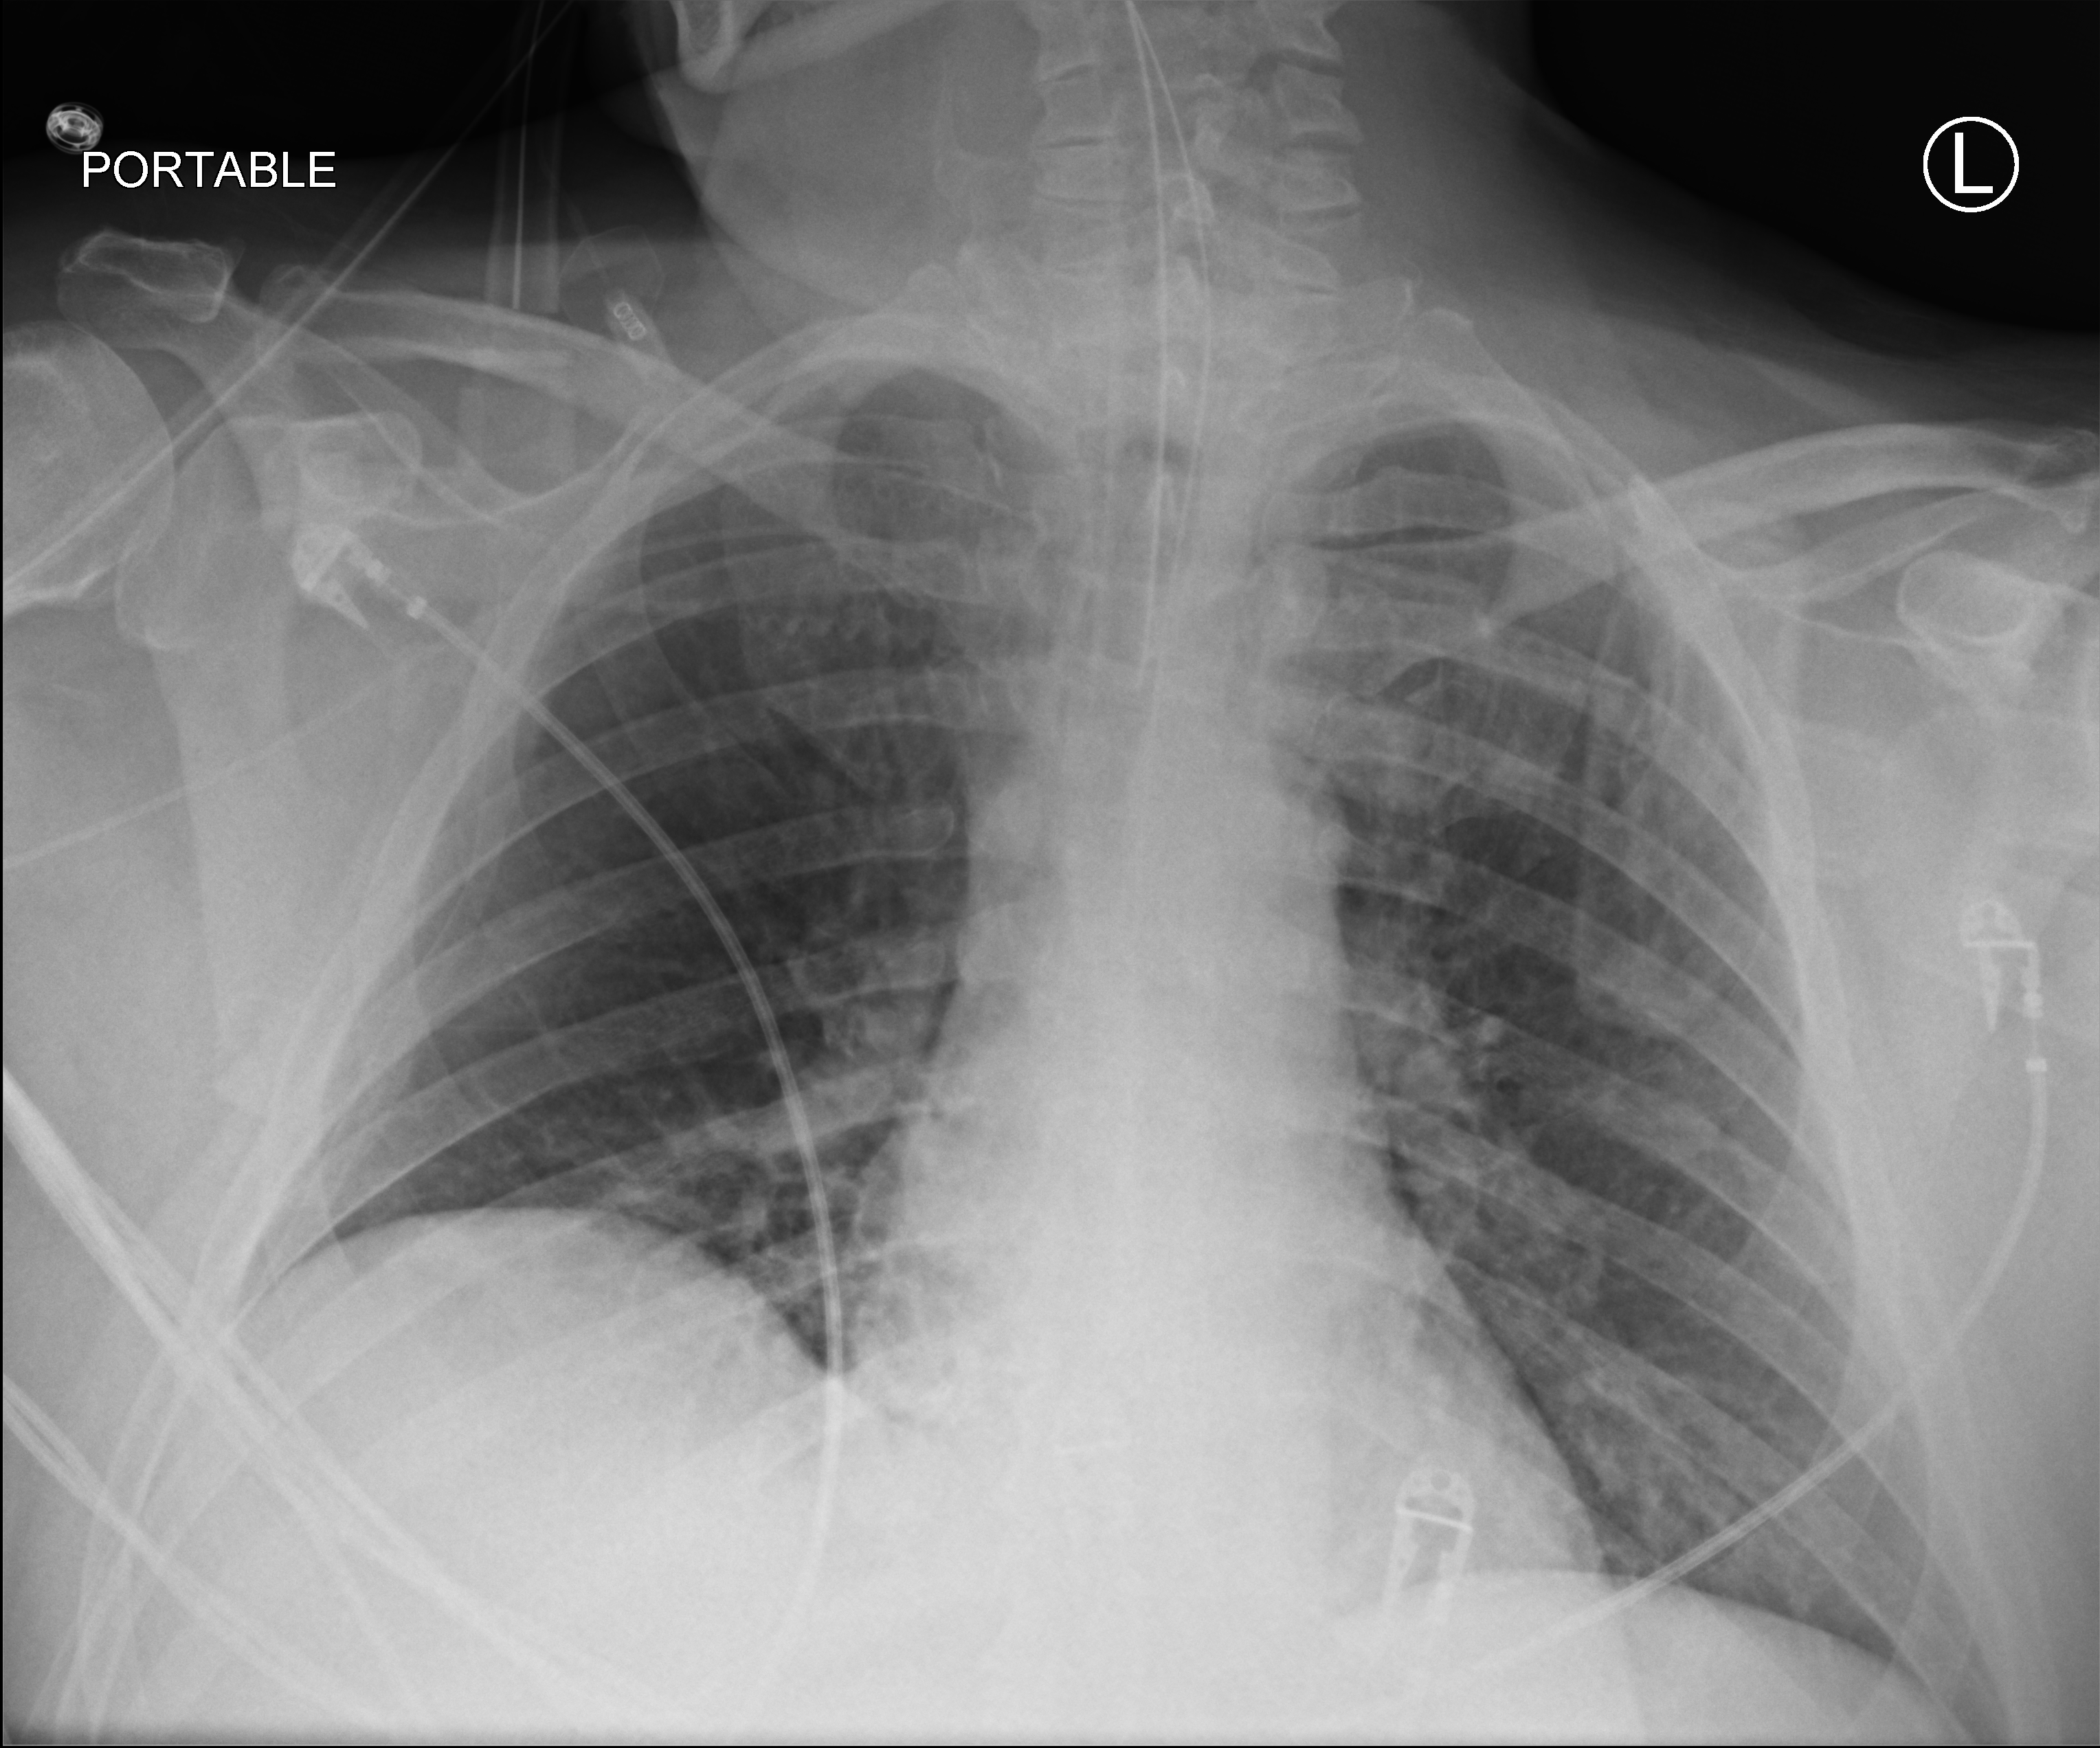
Portable chest radiograph, anteroposterior (AP) projection. Patient hospitalised with COVID-19; male, aged 18–59 years.
Hospital-stay facts (about this admission, not read from this image; timing relative to this image not recorded):
- mechanically ventilated during this hospital stay: yes
- admitted to intensive care during this hospital stay: yes